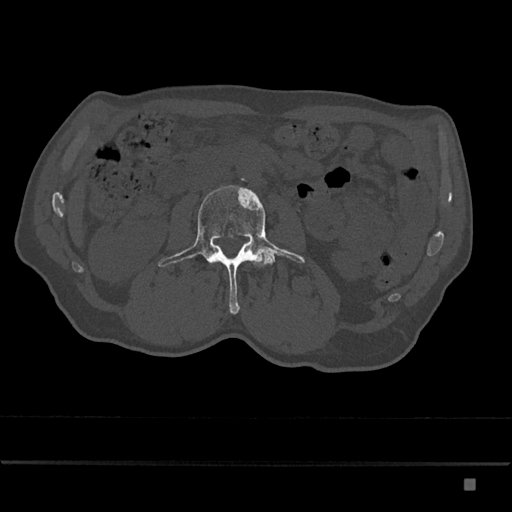
CT including the spine, one axial slice; slice 411 of 797 in the series (ordered by position); bone window (W 1800 / L 400 HU); 512 × 512 image matrix, field of view 390 × 390 mm. Patient: male, 72 years. From the clinical record (not read from this slice): primary cancer: prostate.
Outlined on this slice (semi-automatic segmentation, software-assisted and operator-edited):
- L3 vertebra: bounding box [x1, y1, x2, y2] px = [158, 185, 305, 314]